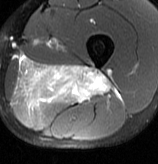
MRI of an extremity soft-tissue mass, one axial slice. Slice 36 of 70 in the series (ordered by position). T2-weighted fat-saturated. MR volume resampled by the dataset authors to the PET/CT grid (not the native acquisition matrix). 158 × 164 image matrix. Male patient. Case-level facts recorded for this patient, not image findings: histological type: extraskeletal osteosarcoma; grade: high; site of the primary tumour: left adductur.
Structures marked on this image (expert contour drawn on MRI and transferred to this co-registered scan by the dataset authors):
- gross tumour volume (mass): bounding box <17,55,116,109> (left, top, right, bottom; pixels)